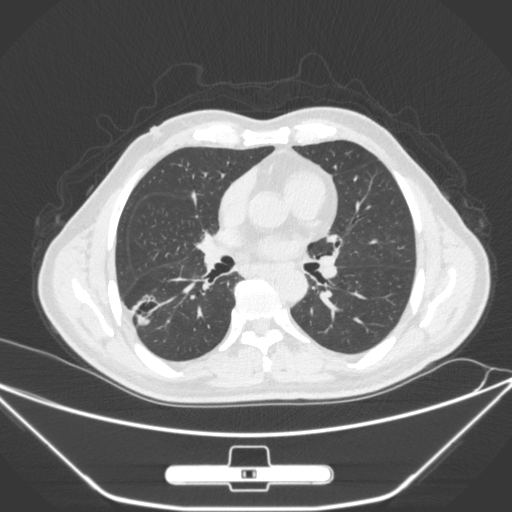
Chest CT, one axial slice. Slice 150 of 310 in the series (ordered by position). Lung window (W 1500 / L -600 HU). 512 × 512 image matrix, field of view 398 × 398 mm. Male patient, age 71 years. Case-level facts recorded for this patient, not image findings: clinical TNM (as recorded): T1c N0 M0.
Outlined on this slice (bounding box drawn by a radiologist):
- lung tumour (recorded histology: adenocarcinoma): bounding box (x1, y1, x2, y2) in pixels: (130, 286, 160, 330)